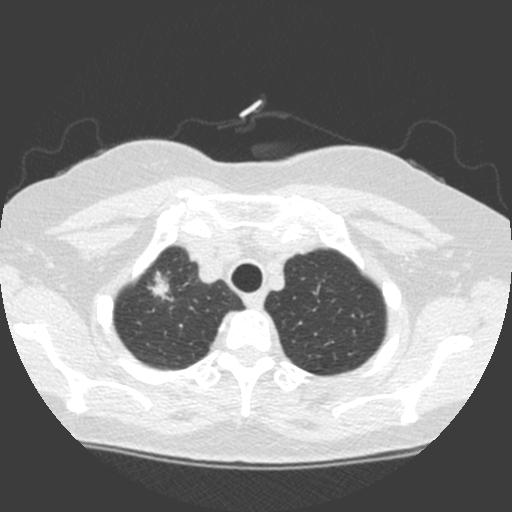
Axial slice from a low-dose chest CT screening exam; baseline screening round; lung window (W 1500 / L -600 HU); 2 mm slice thickness; standard (soft-tissue) reconstruction kernel (C); slice 17 of 155 in the series. Female participant, aged 63 years at enrolment. Current smoker at enrolment.
Lesion marked by an expert reader, box from (x=134, y=266) to (x=183, y=309) px. Reader record for this screening exam (exam-level; its link to the box is not recorded): non-calcified nodule or mass ≥4 mm, right upper lobe, 11 × 11 mm, spiculated (stellate) margins, soft tissue attenuation. Later outcome: lung cancer diagnosed 6 days after this screen — adenocarcinoma, NOS, right upper lobe, poorly differentiated (G3), stage IA (AJCC 6th edition), 17 mm at pathology.